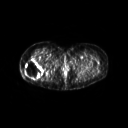
FDG PET of an extremity soft-tissue mass (from a PET/CT study), one axial slice; slice 34 of 267 in the series (ordered by position); 3.27 mm slice thickness; 128 × 128 image matrix, field of view 600 × 600 mm. Female patient, age 57 years. Case-level facts recorded for this patient, not image findings: histological type: epithelioid sarcoma with vascular differentiation; site of the primary tumour: right buttock.
Annotated regions visible in this slice (expert contour drawn on MRI and transferred to this co-registered scan by the dataset authors):
- gross tumour volume (mass): box from (x=24, y=59) to (x=43, y=79) px